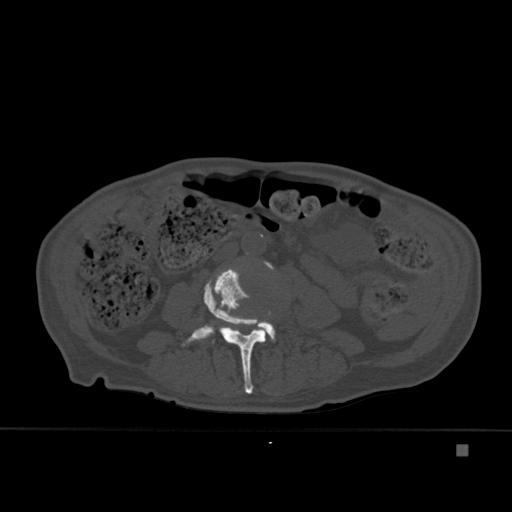
CT including the spine, one axial slice. Slice 138 of 451 in the series (ordered by position). Bone window (W 1800 / L 400 HU). 512 × 512 image matrix. Male patient, age 75 years. From the clinical record (not read from this slice): primary cancer: prostate.
Structures marked on this image (semi-automatic segmentation, software-assisted and operator-edited):
- L3 vertebra: box from (x=181, y=268) to (x=271, y=394) px
- L4 vertebra: (x=219, y=261)–(x=276, y=342)